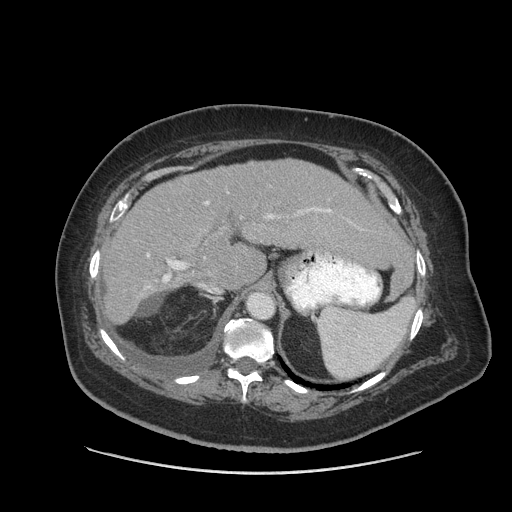
Contrast-enhanced abdominal CT (liver protocol), one axial slice; slice 57 of 91 in the series (ordered by position); soft-tissue window (W 400 / L 40 HU); 2.5 mm slice thickness; 512 × 512 image matrix, field of view 420 × 420 mm. From the clinical record (not read from this slice): diagnosis: hepatocellular carcinoma (patient treated with transarterial chemoembolisation; whether this scan precedes or follows treatment is not stated here); TNM stage (as recorded): Stage-I; Child-Pugh class: A; tumour nodularity: uninodular.
Annotated regions visible in this slice (semi-automatic segmentation, software-assisted and operator-edited):
- liver parenchyma outside the tumour (the mass and vessels are separate outlines, so this box may not span the whole liver): bounding box <100,158,403,322> (left, top, right, bottom; pixels)
- liver vessels: <147,201,331,282>